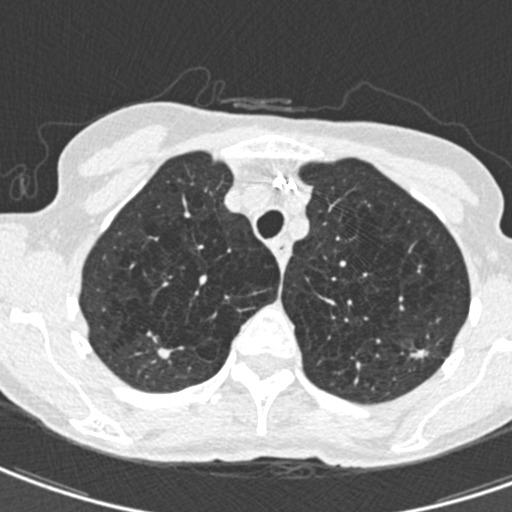
Axial slice from a low-dose chest CT screening exam; second annual screen; lung window (W 1500 / L -600 HU); standard (soft-tissue) reconstruction kernel (B30f); 512 × 512 image matrix. Female participant, aged 71 years at enrolment. Current smoker at enrolment.
Expert-annotated lung lesion, bounding box <405,332,444,370> (left, top, right, bottom; pixels). The screening reader recorded 2 non-calcified nodules or masses ≥4 mm on this exam (right upper lobe, left upper lobe); which of them this box marks is not recorded. Official screen result: positive, change unspecified: nodule(s) >= 4 mm or enlarging nodule(s), mass(es), or other non-specific abnormalities suspicious for lung cancer. Later outcome: lung cancer diagnosed 604 days after this screen — adenocarcinoma, NOS, left upper lobe, moderately differentiated (G2), stage IA (AJCC 6th edition), 12 mm at pathology.